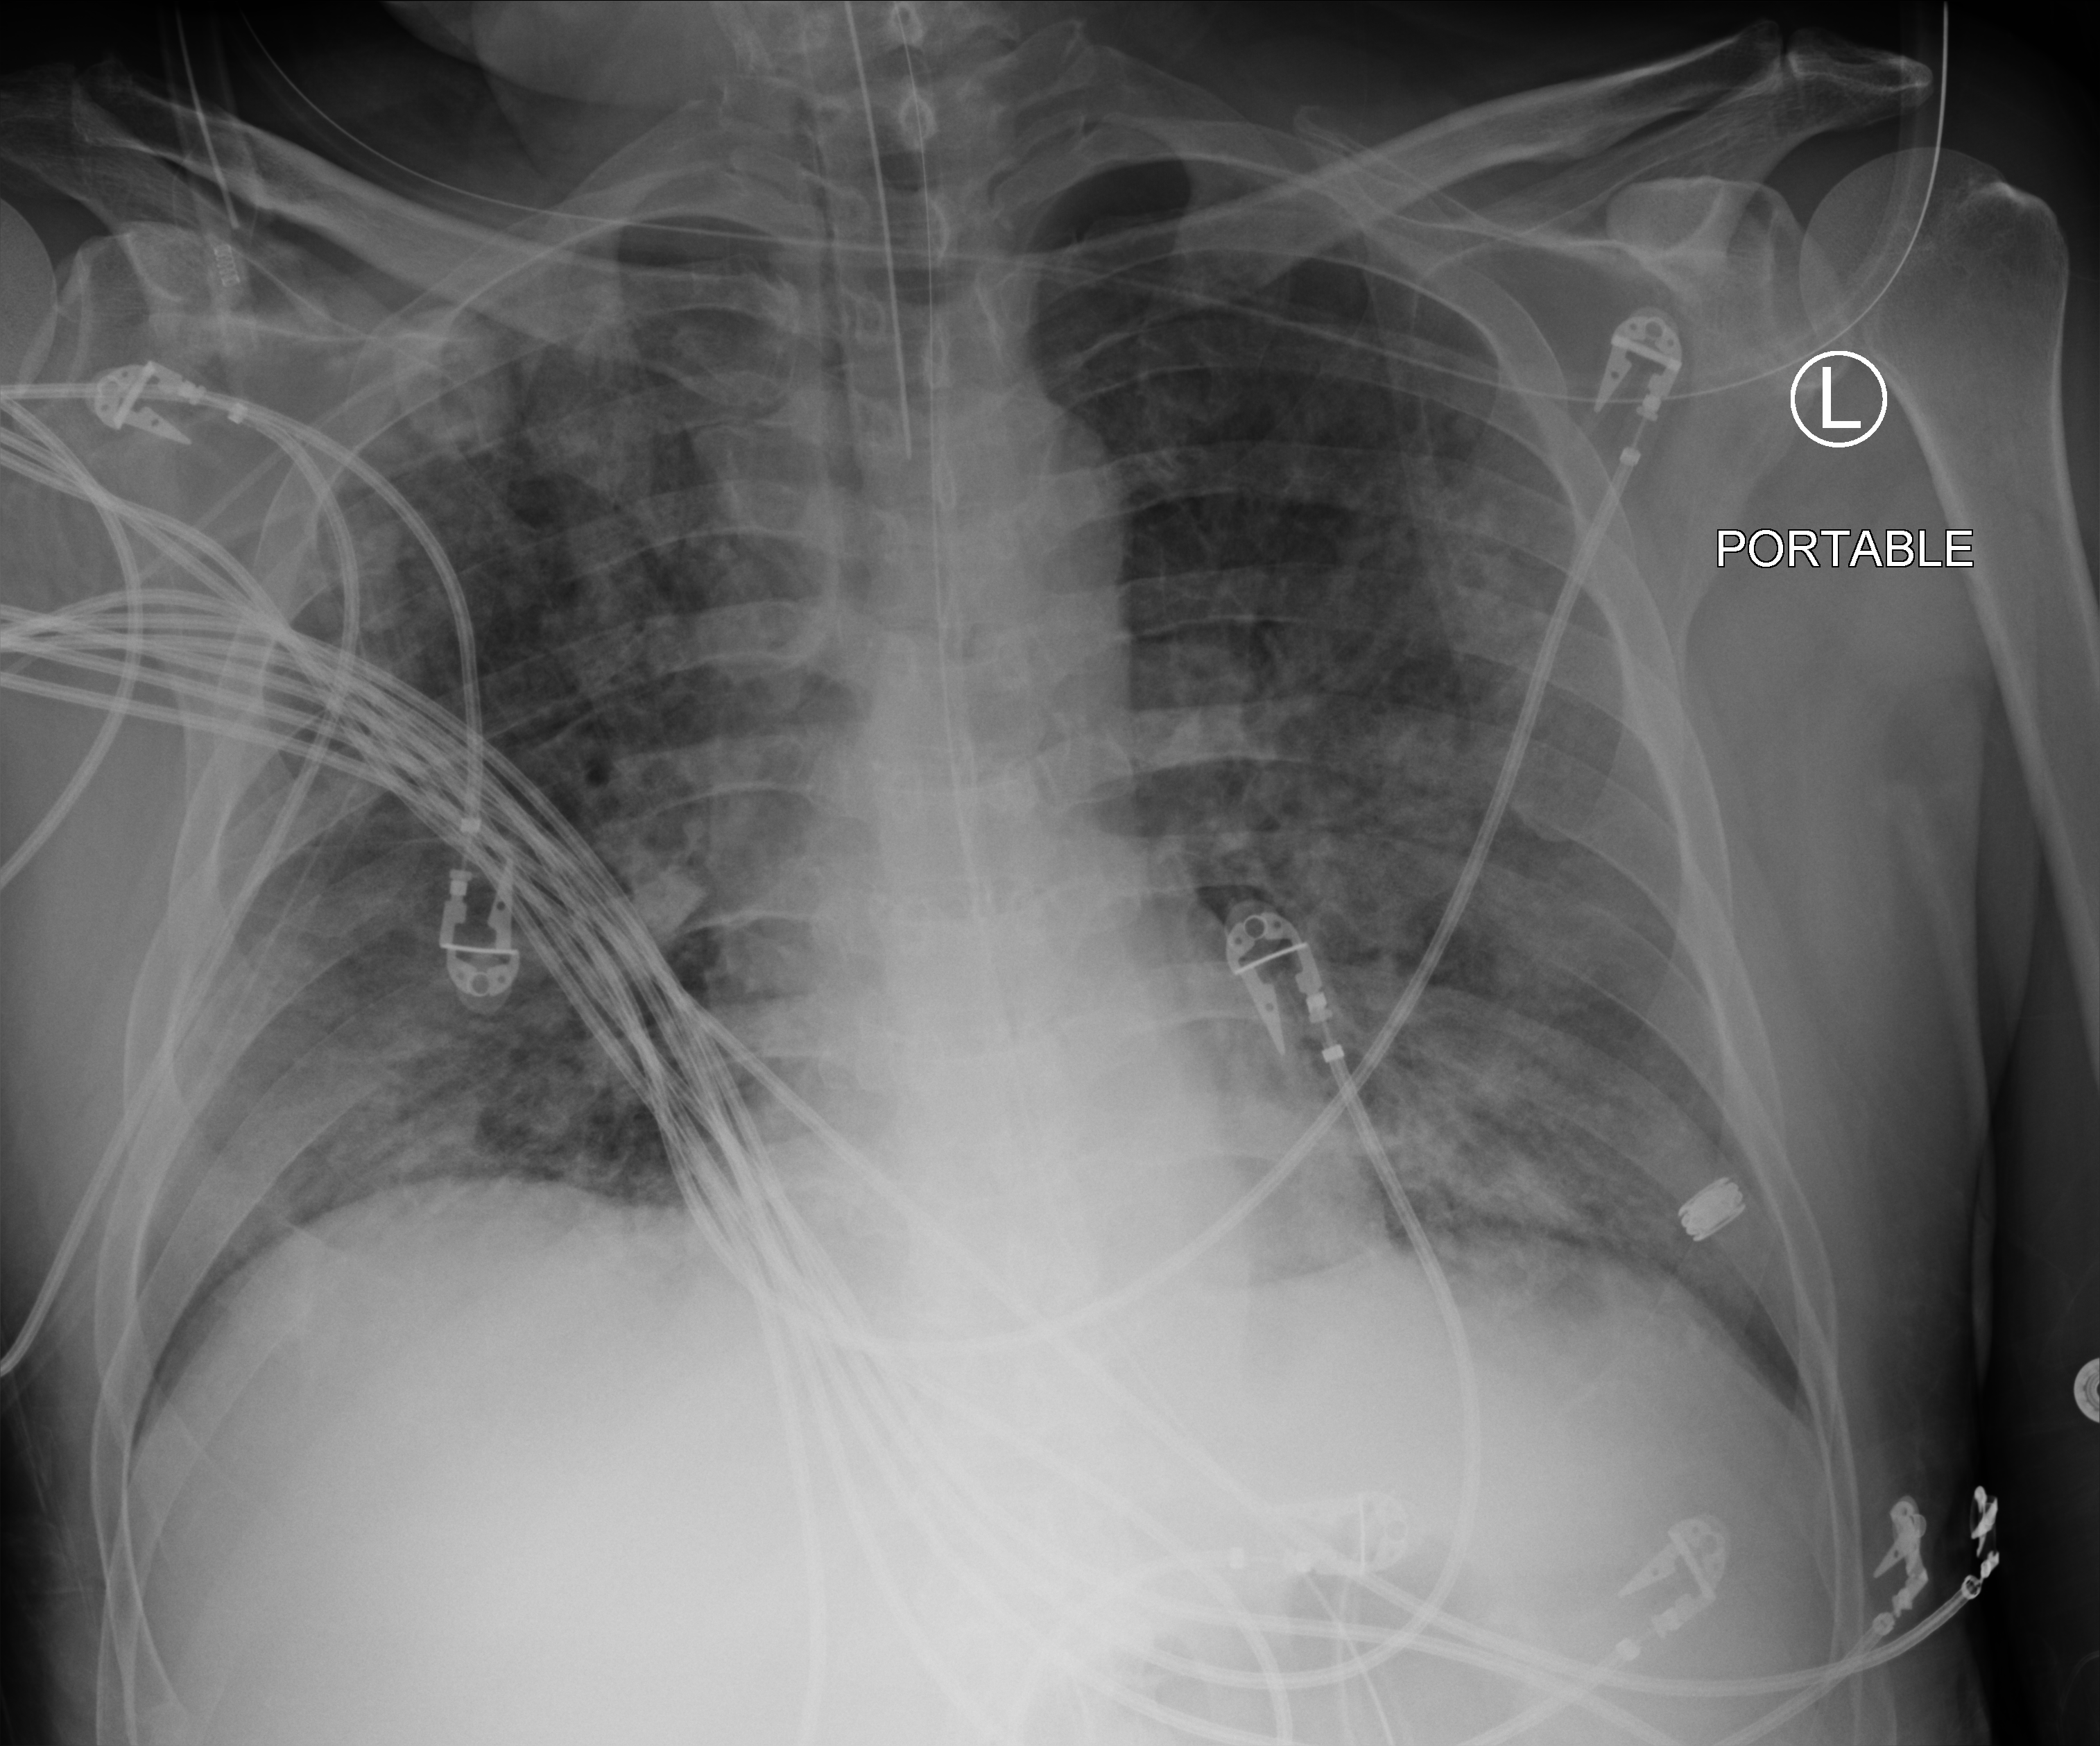
Bedside chest radiograph (computed radiography), anteroposterior (AP) projection. Male patient hospitalised with COVID-19, age 18–59 years.
From the hospital-stay record, not from the radiograph (when in the stay this image was taken is not recorded): chronic kidney disease (admission record): no; smoking status (admission record): former.